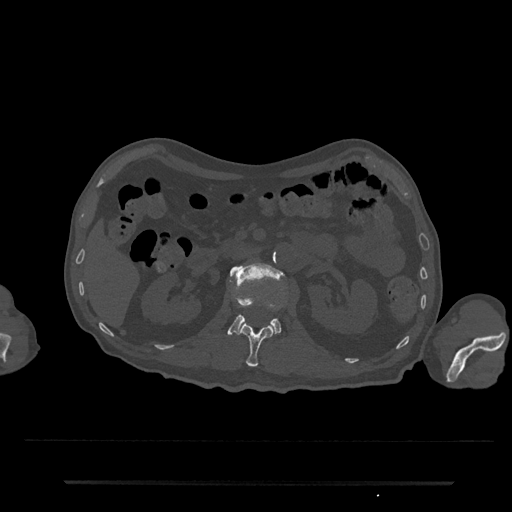
CT including the spine, one axial slice; position 100 of 797 along the scan axis; reconstruction kernel Br40s/3; 120 kVp; bone window (W 1800 / L 400 HU); 0.5 mm slice thickness; 512 × 512 image matrix. Male patient, age 74 years. Case-level facts recorded for this patient, not image findings: primary cancer: prostate.
Annotated regions visible in this slice (semi-automatically segmented with operator editing):
- L1 vertebra: bounding box (x1, y1, x2, y2) in pixels: (239, 323, 274, 367)
- L2 vertebra: (228, 262, 283, 335)